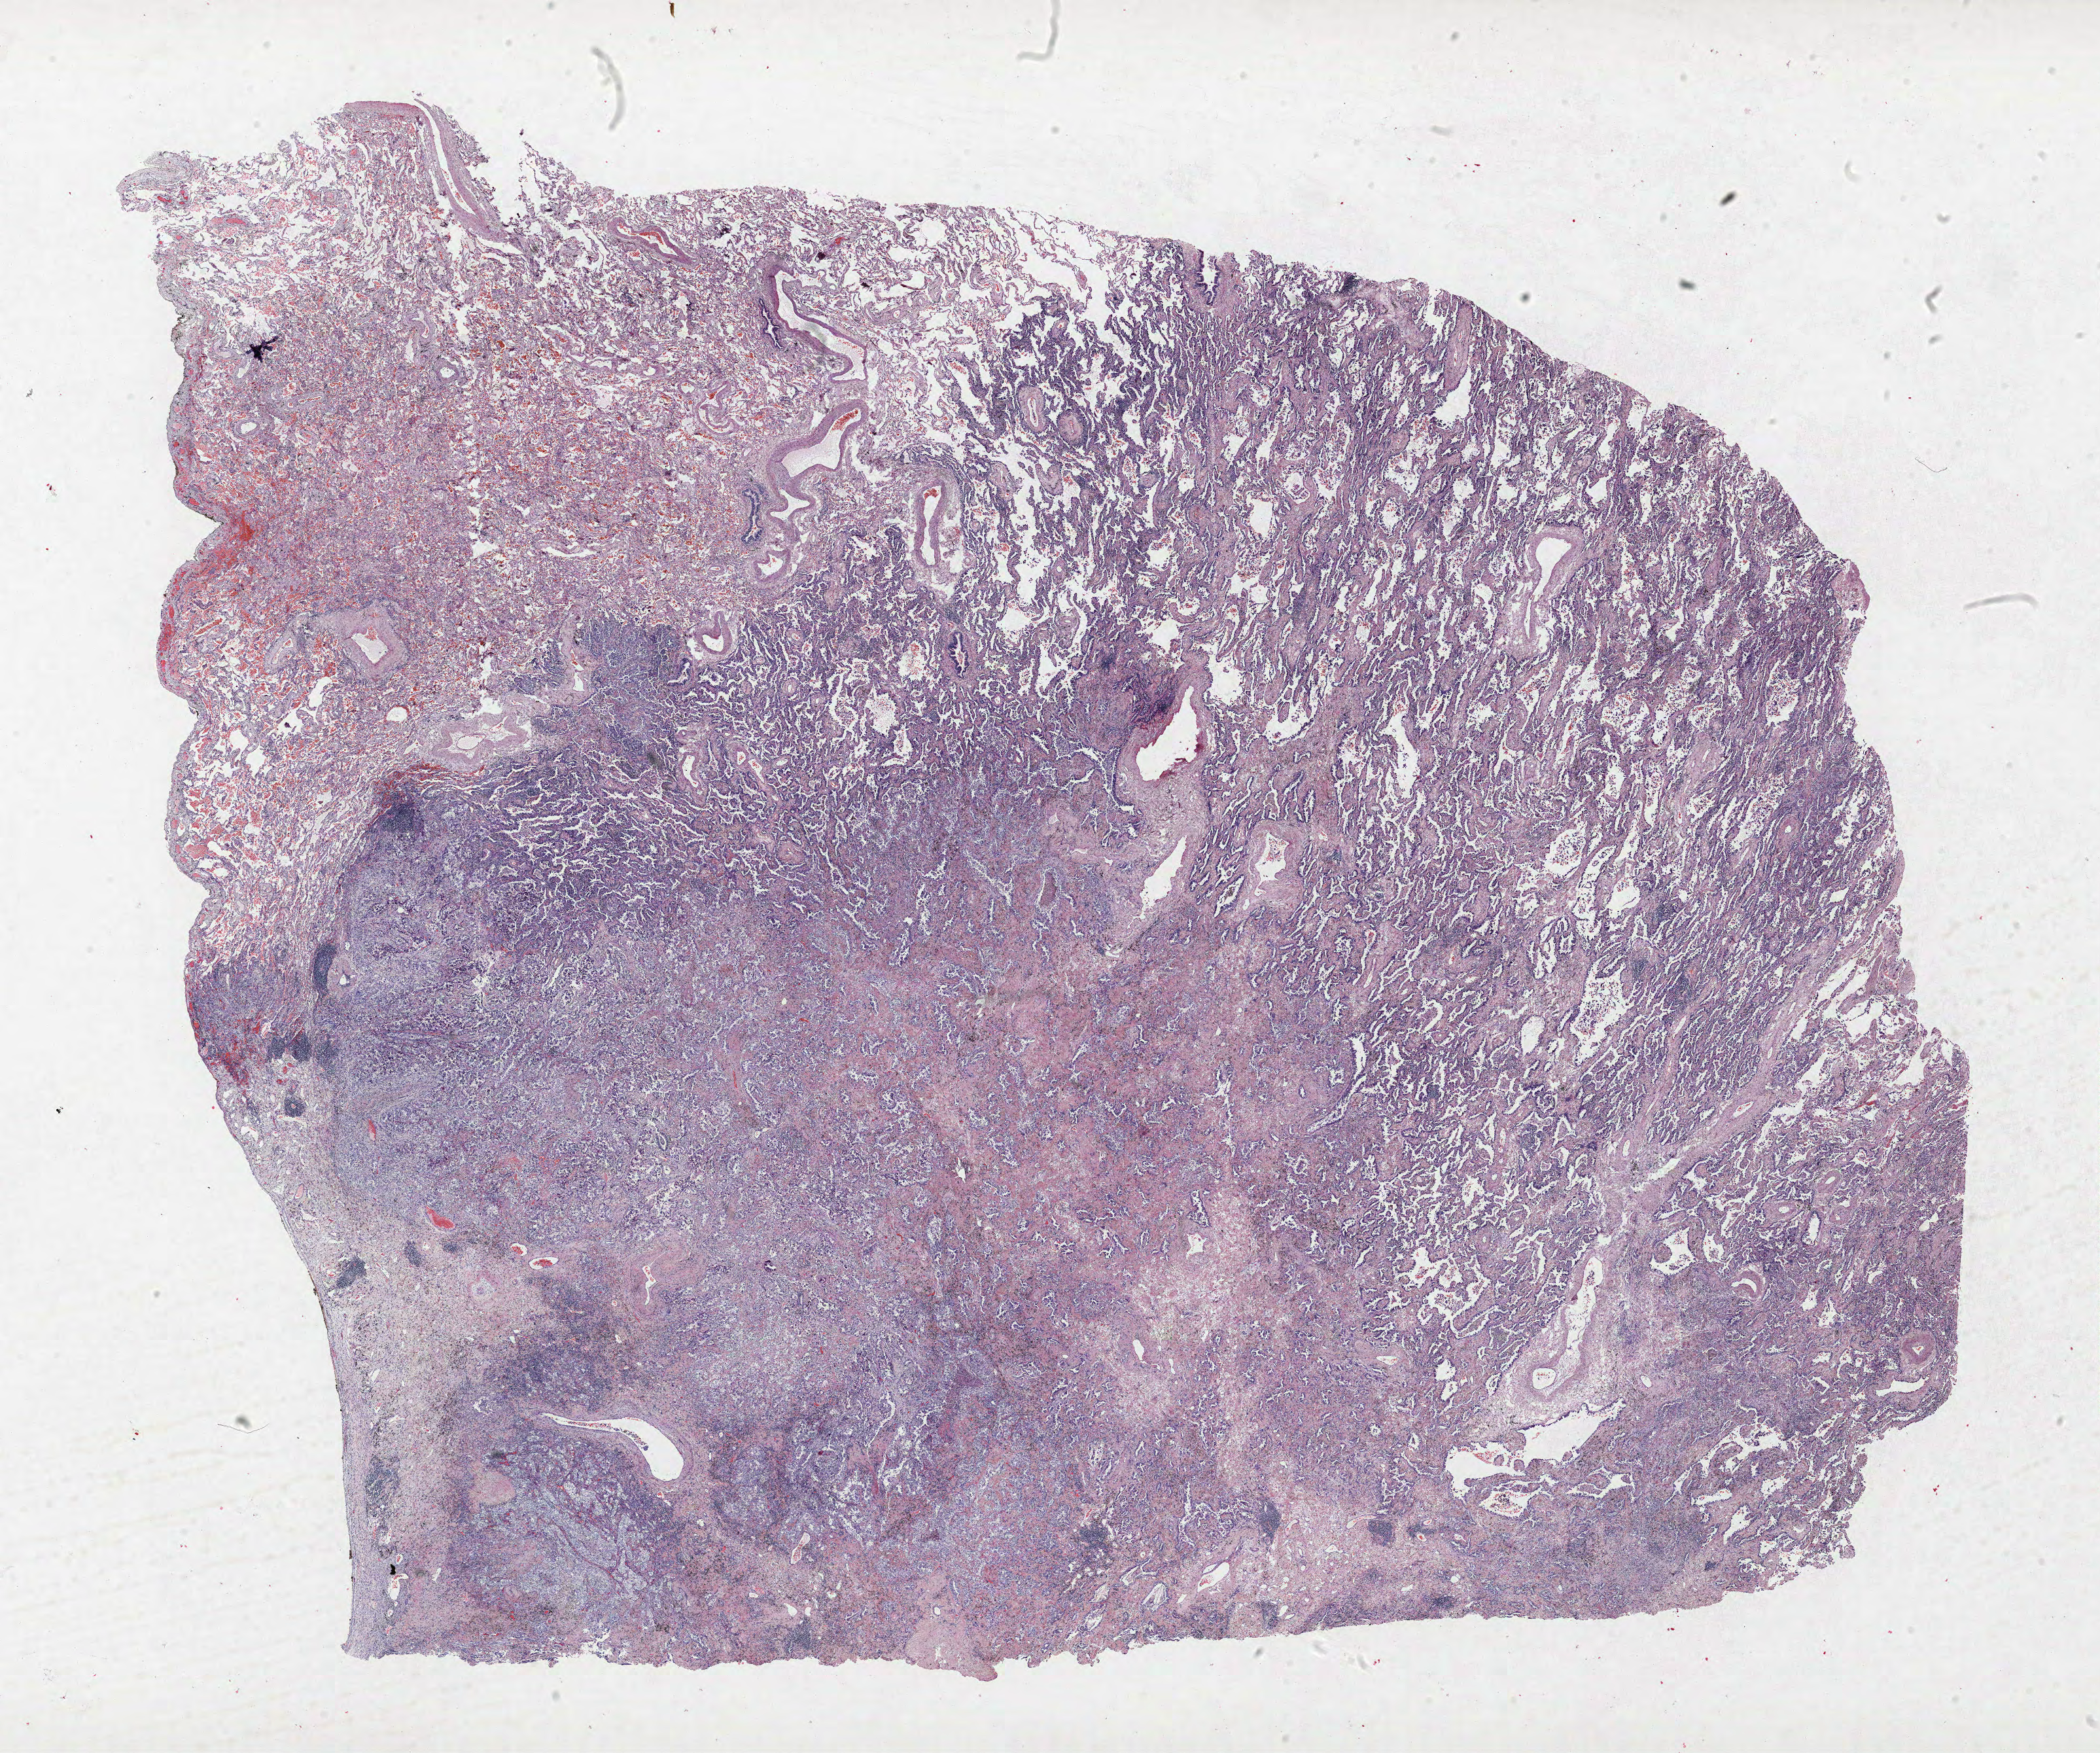
H&E-stained whole-slide image, low-resolution overview of the scanned area, about 25.7 x 21.4 mm (slide scanned at 40x). FFPE section. Lung tissue. Female patient, aged 70 at enrolment. Former smoker at enrolment. Grade: moderately differentiated (G2).
Tumour size (pathology): 41 mm. Participant's lung-cancer diagnosis: Clear cell adenocarcinoma, NOS. Stage (AJCC 6th edition): IB. Primary tumour location (clinical record): left upper lobe. ICD-O-3 topography: upper lobe of lung (C34.1).